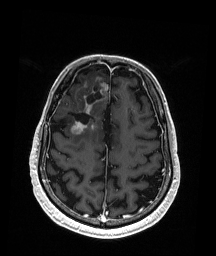
Brain MRI from a brain-tumour surgery series, one axial slice. Slice 58 of 192 in the series (ordered by position). T1-weighted post-contrast. 1 mm slice thickness. 216 × 256 image matrix, field of view 211 × 250 mm. Case-level facts recorded for this patient, not image findings: histopathology: Astrocytoma; WHO grade: 3; IDH mutation: yes; tumour location: Right Frontal.
Annotated regions visible in this slice (expert manual segmentation):
- previous resection cavity: box from (x=69, y=87) to (x=102, y=124) px
- tumour: (x=70, y=84)–(x=109, y=137)